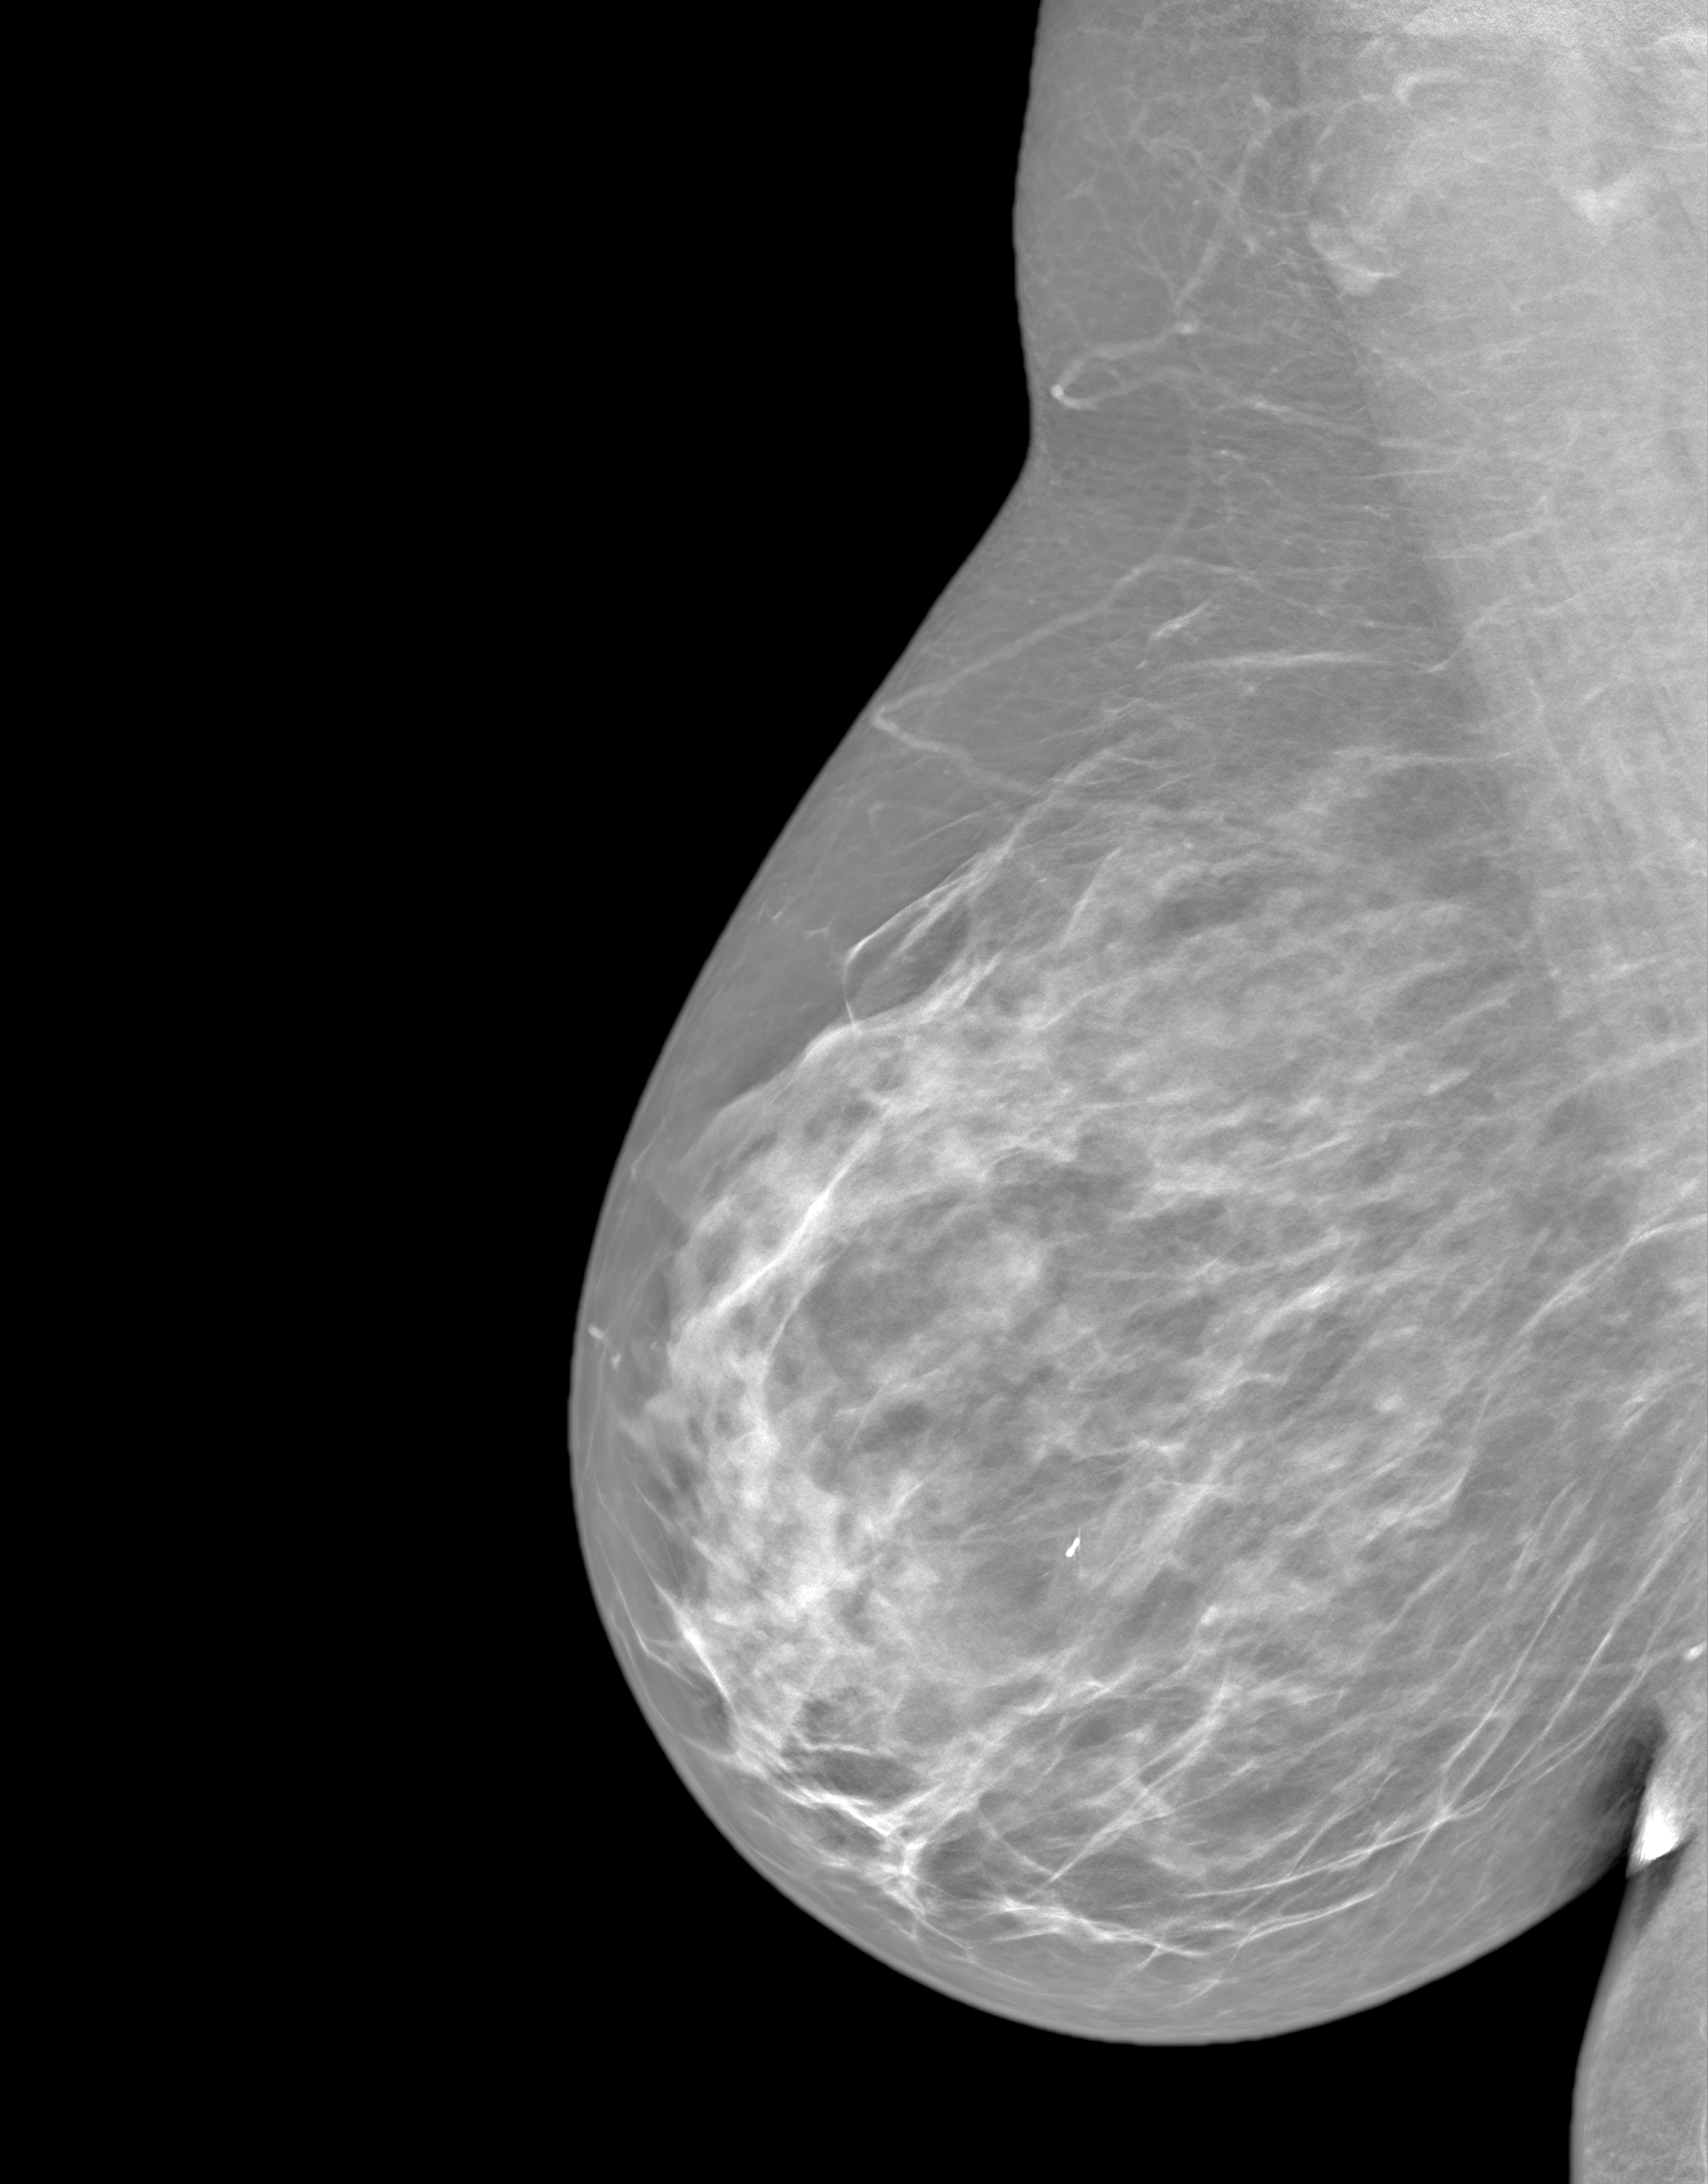
Screening examination; system: SenoIris_1SP2(440). Female patient, age 43 years.
Image type: synthesized 2-D view from tomosynthesis. Breast: right. Projection: mediolateral oblique (MLO) view.